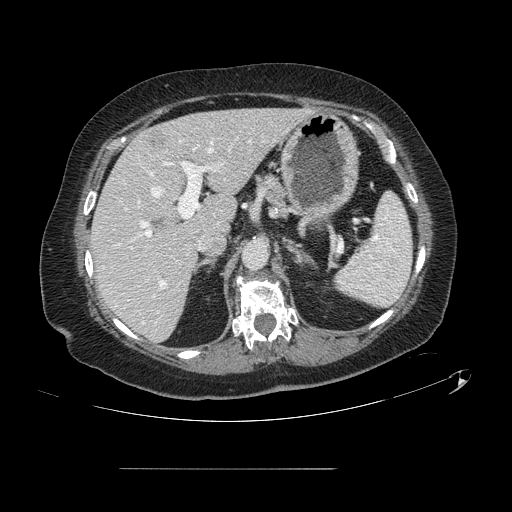
Contrast-enhanced abdominal CT, one axial slice; slice 81 of 148 in the series (ordered by position); 120 kVp; intravenous contrast given; soft-tissue window (W 400 / L 40 HU); 512 × 512 image matrix, field of view 439 × 439 mm. Female patient, age 75 years. Case-level facts recorded for this patient, not image findings: diagnosis: colorectal cancer liver metastases, imaged before liver resection; multiple liver metastases: no; largest metastasis: 2.4 cm.
Outlined on this slice (expert manual segmentation):
- hepatic veins: box from (x=152, y=143) to (x=213, y=197) px
- liver: (x=92, y=108)–(x=307, y=342)
- planned liver remnant (the part of the liver to remain after resection): (x=92, y=109)–(x=306, y=342)
- portal vein (with intrahepatic branches): (x=132, y=139)–(x=265, y=288)
- liver metastasis: (x=147, y=131)–(x=167, y=147)